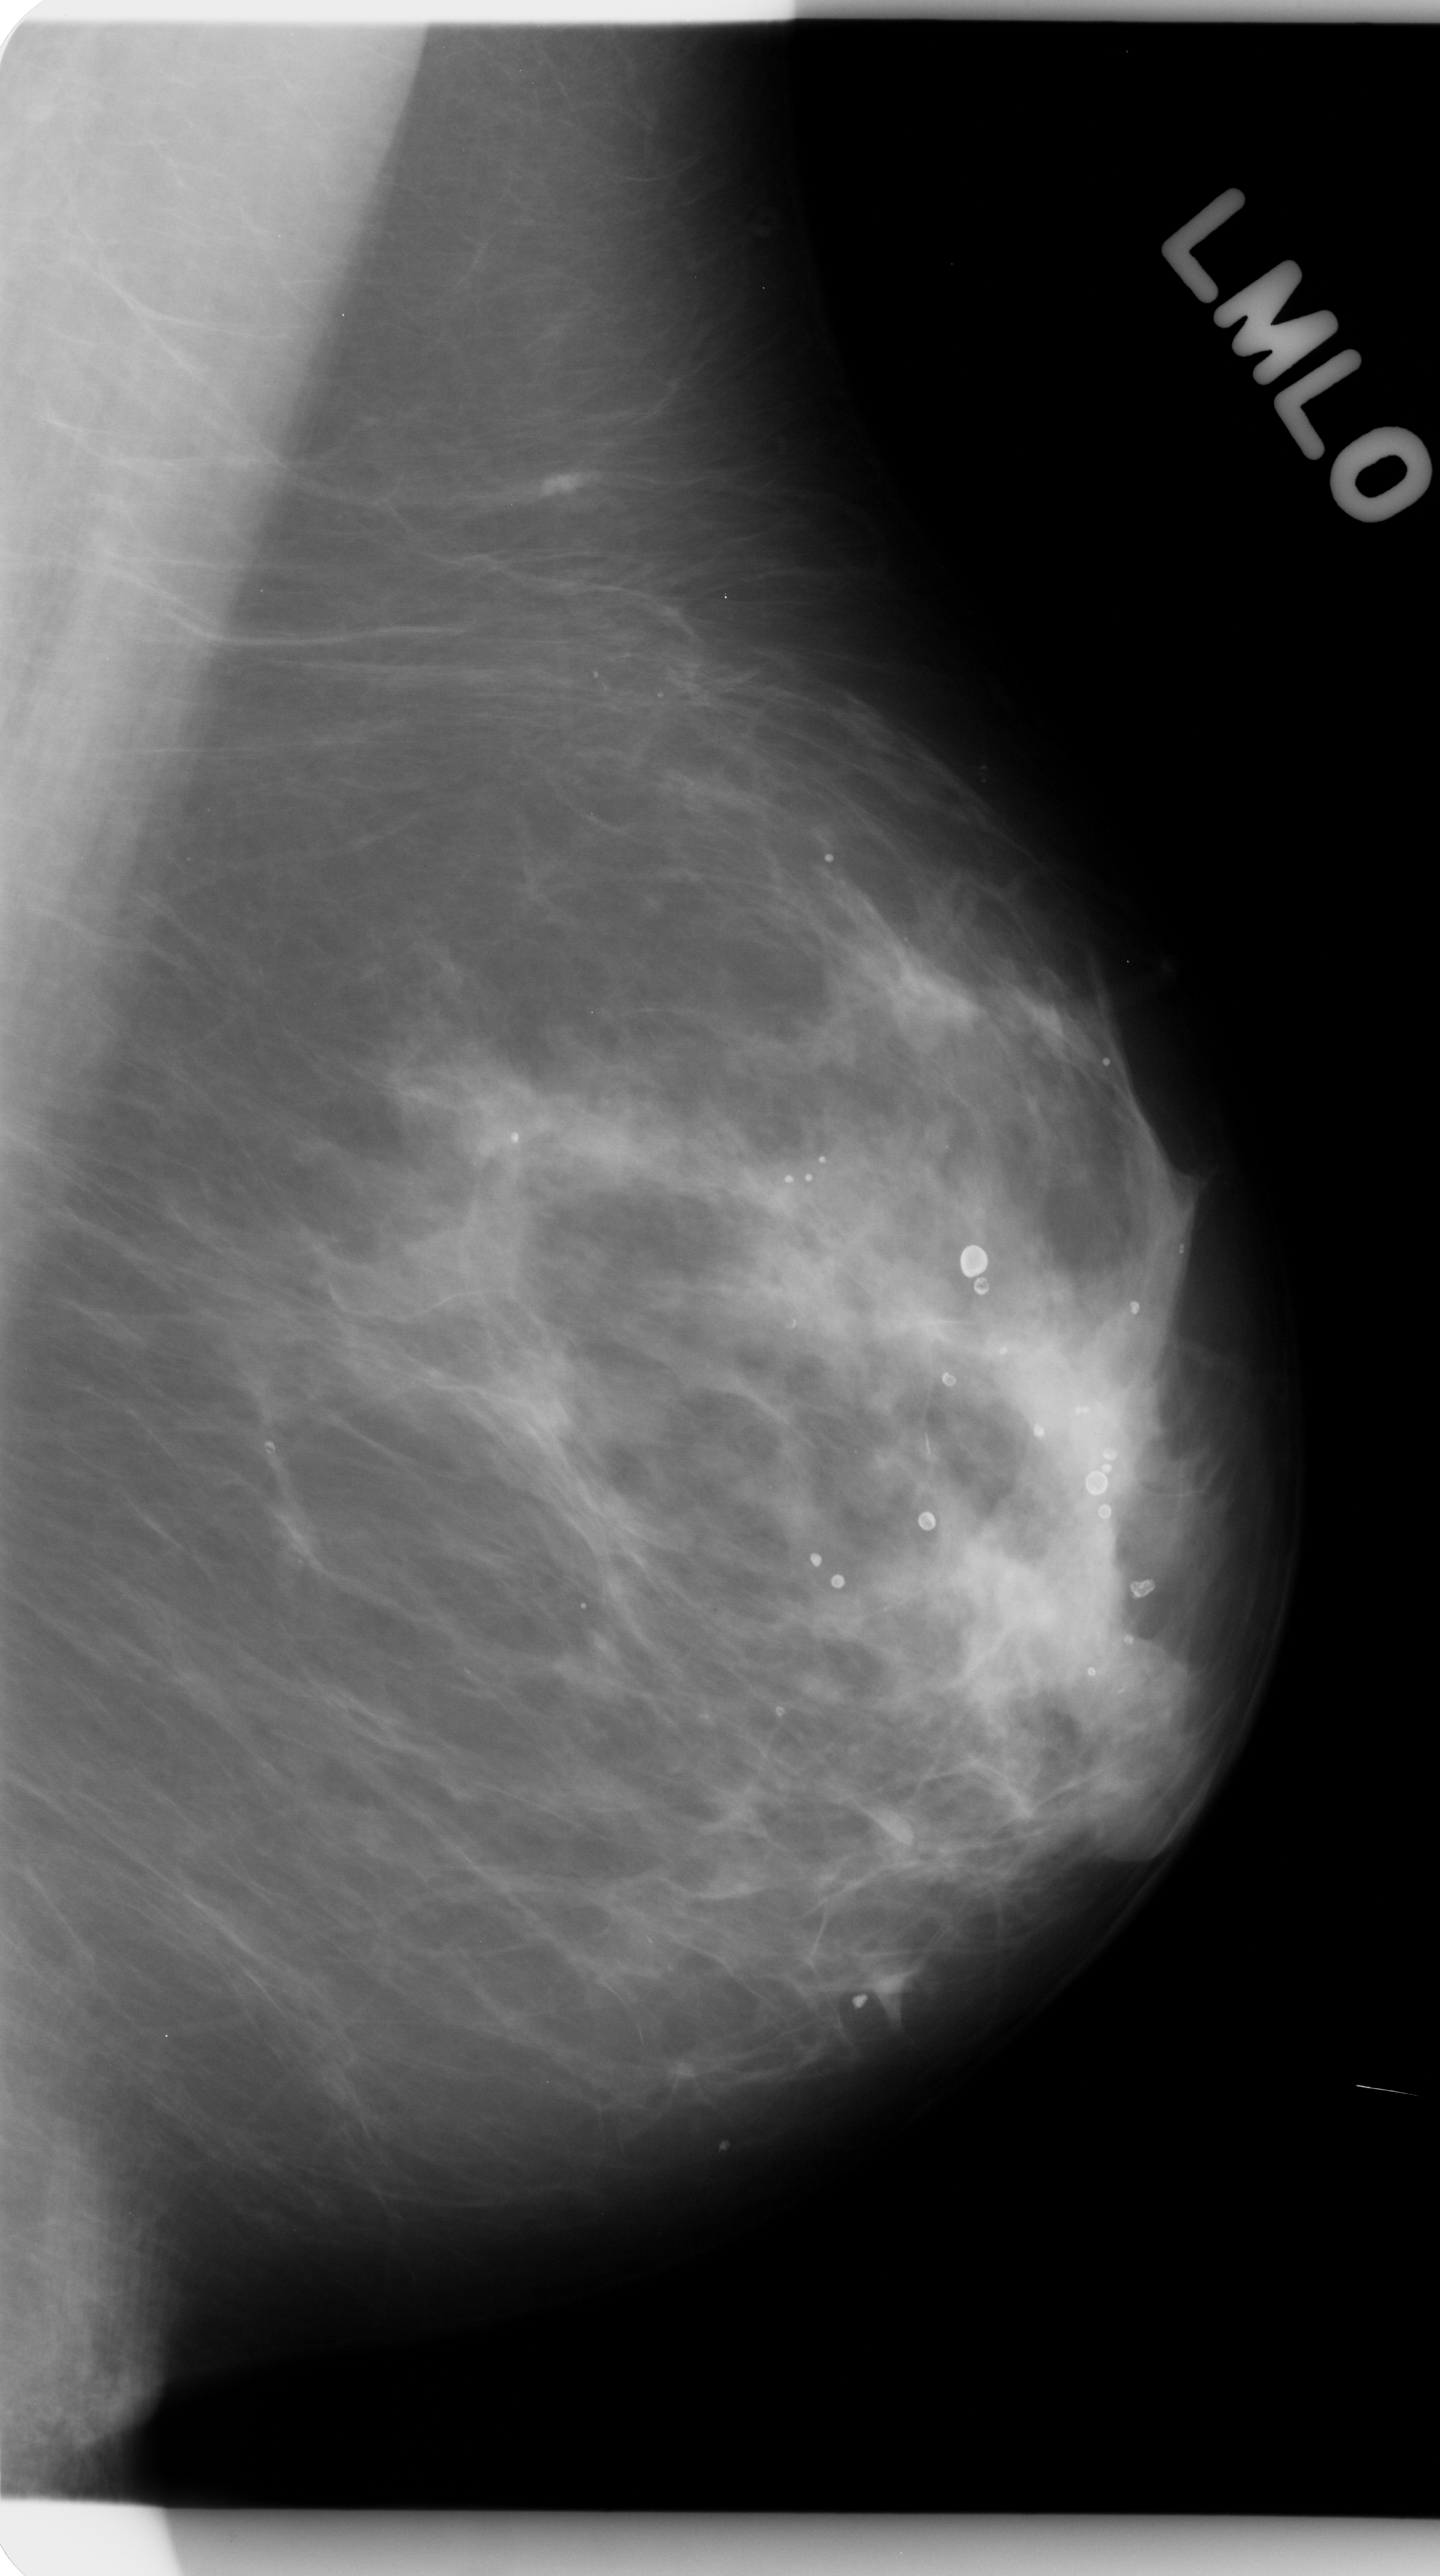
Digitized screen-film mammogram; left breast; MLO view; breast composition: scattered fibroglandular densities (BI-RADS density category 2 of 4); 1440 × 2576 image matrix.
Expert-marked regions of interest on this film, with their recorded descriptors:
- mass, shape architectural distortion, margins spiculated; BI-RADS assessment category 4; pathology (as recorded): benign: bounding box (x1, y1, x2, y2) in pixels: (867, 1268, 1009, 1402)